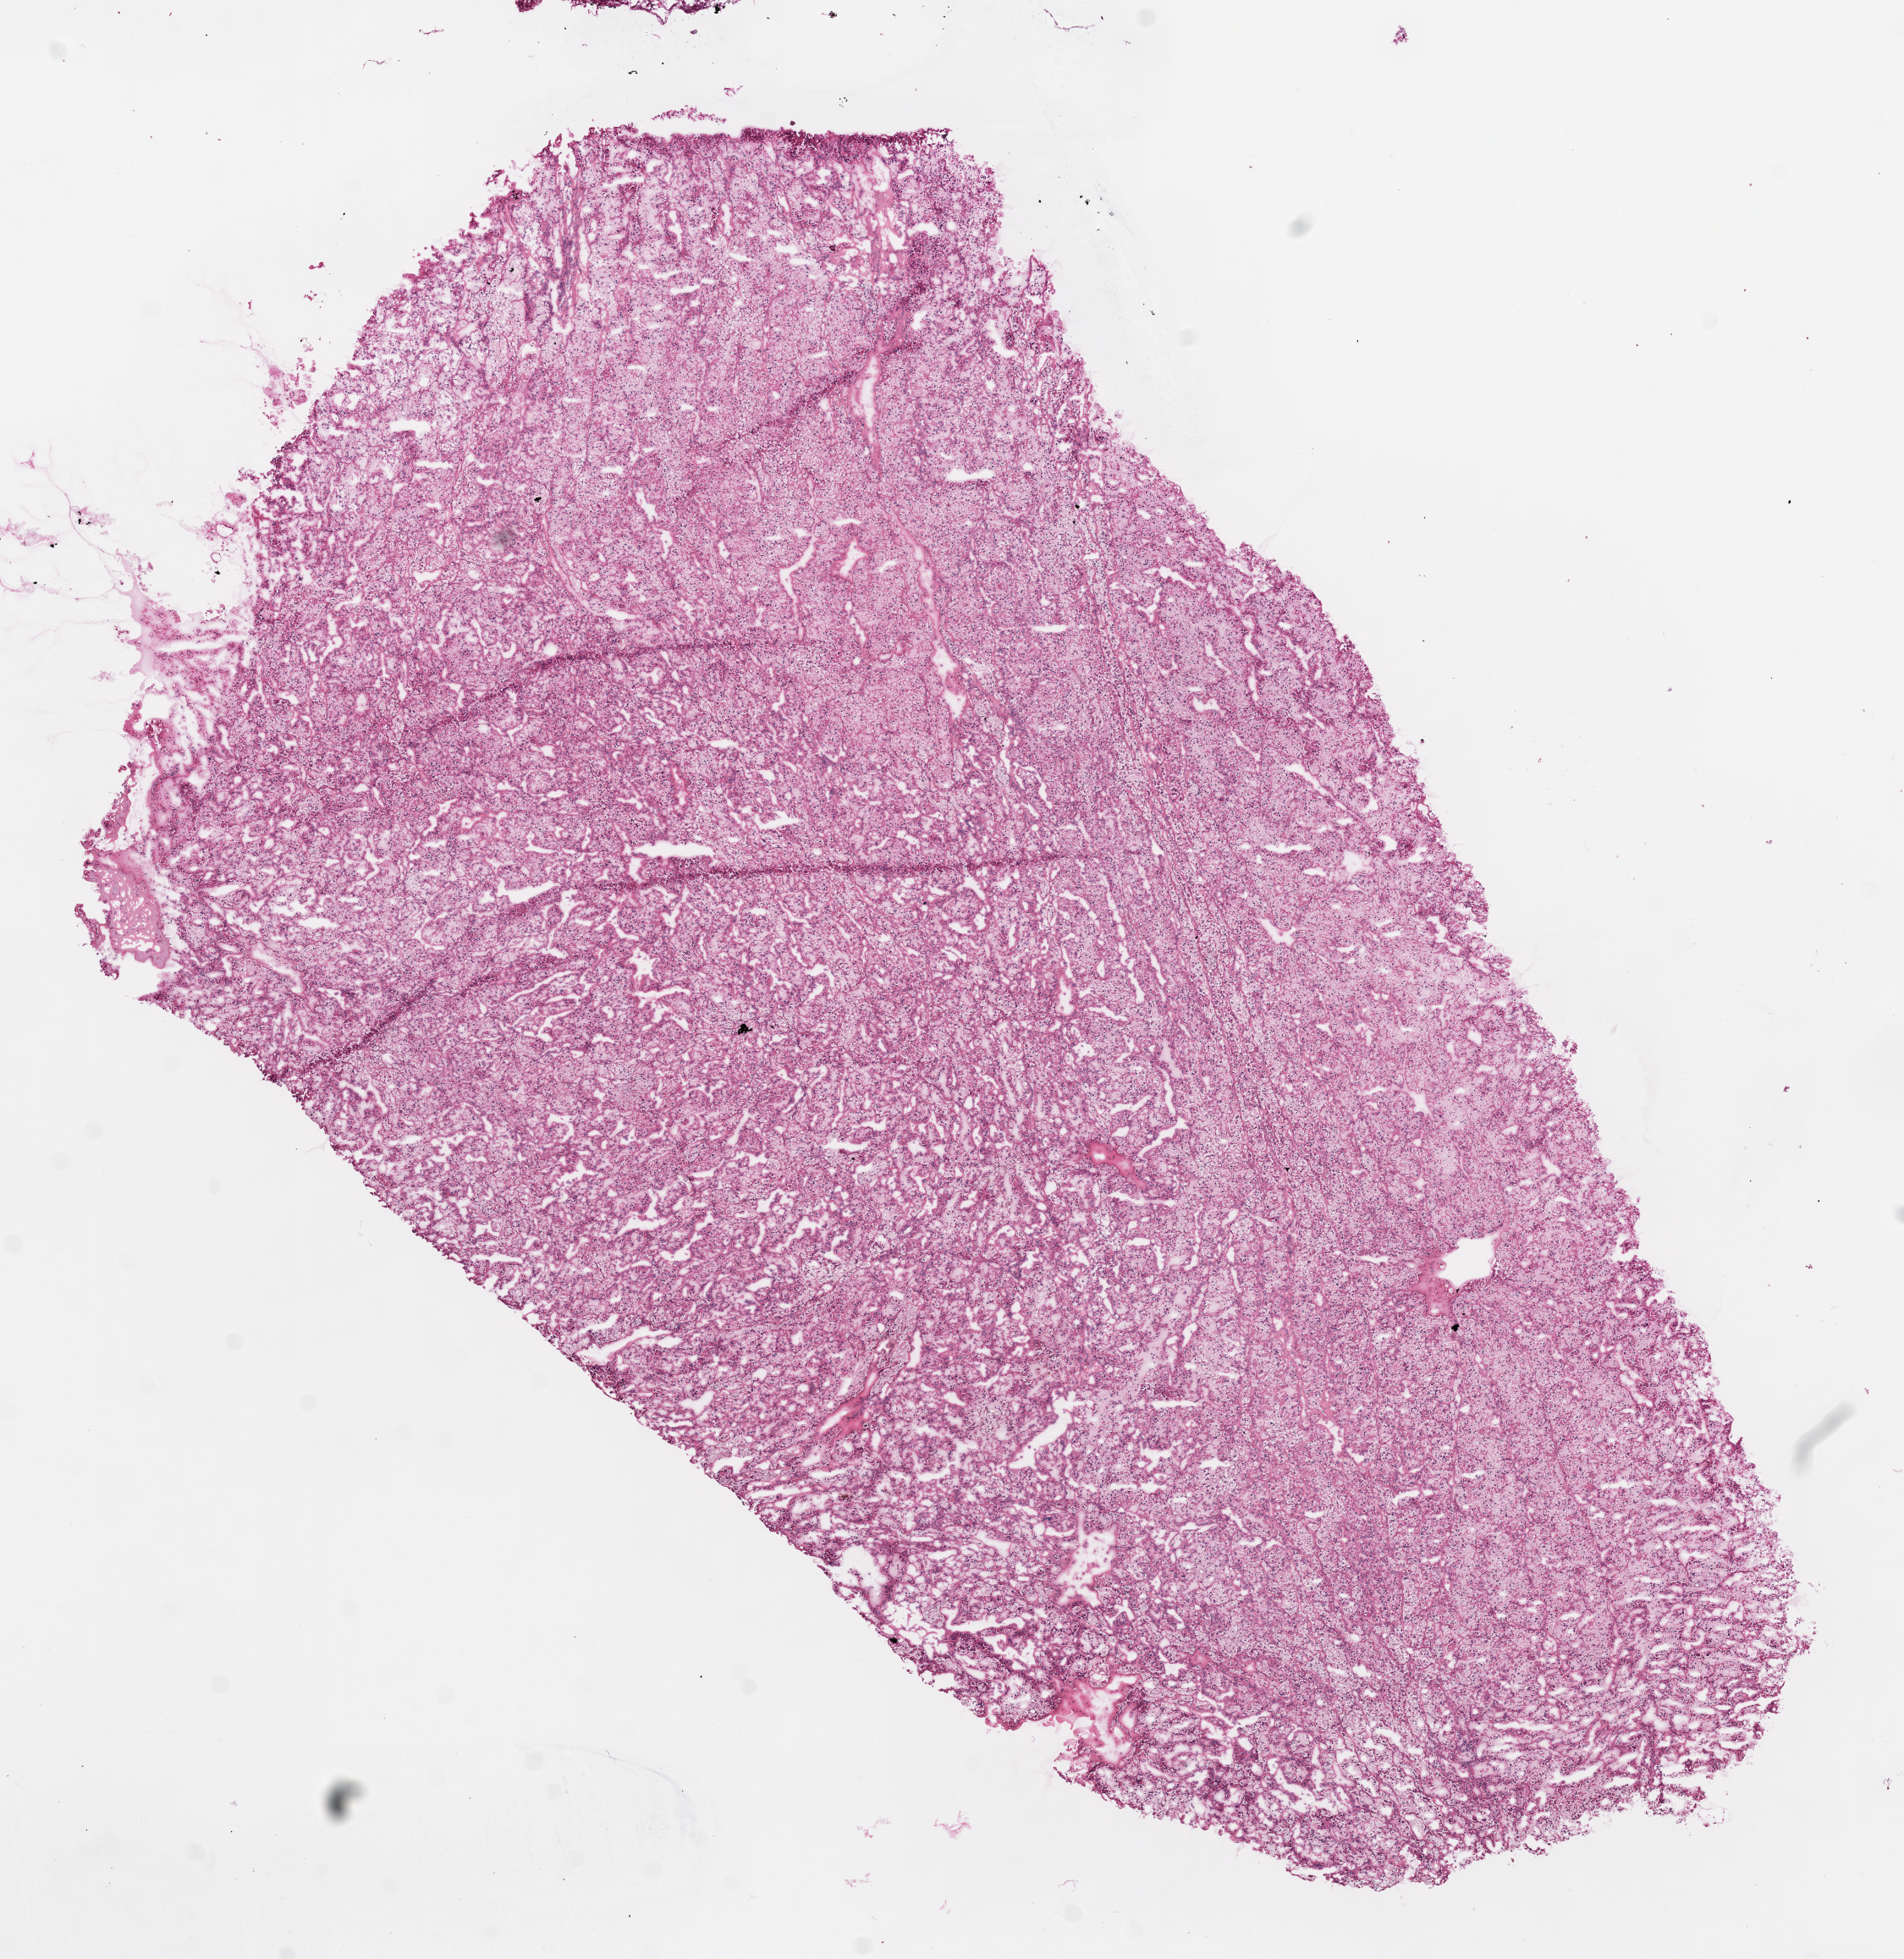
Hematoxylin and eosin (H&E) stained whole-slide image, whole scanned area (about 9.0 x 9.3 mm) shown as a low-resolution overview, frozen section, primary tumour sample from the kidney. Patient: male, age at initial diagnosis 61 years. Histologic grade: G3 (poorly differentiated). Pathologist review of this section (percent, as recorded): tumour cells 95%, tumour nuclei 85%, normal cells 0%, stromal cells 5%, necrosis 0%.
Pathologic diagnosis: Clear cell adenocarcinoma, NOS. AJCC pathologic stage: III.